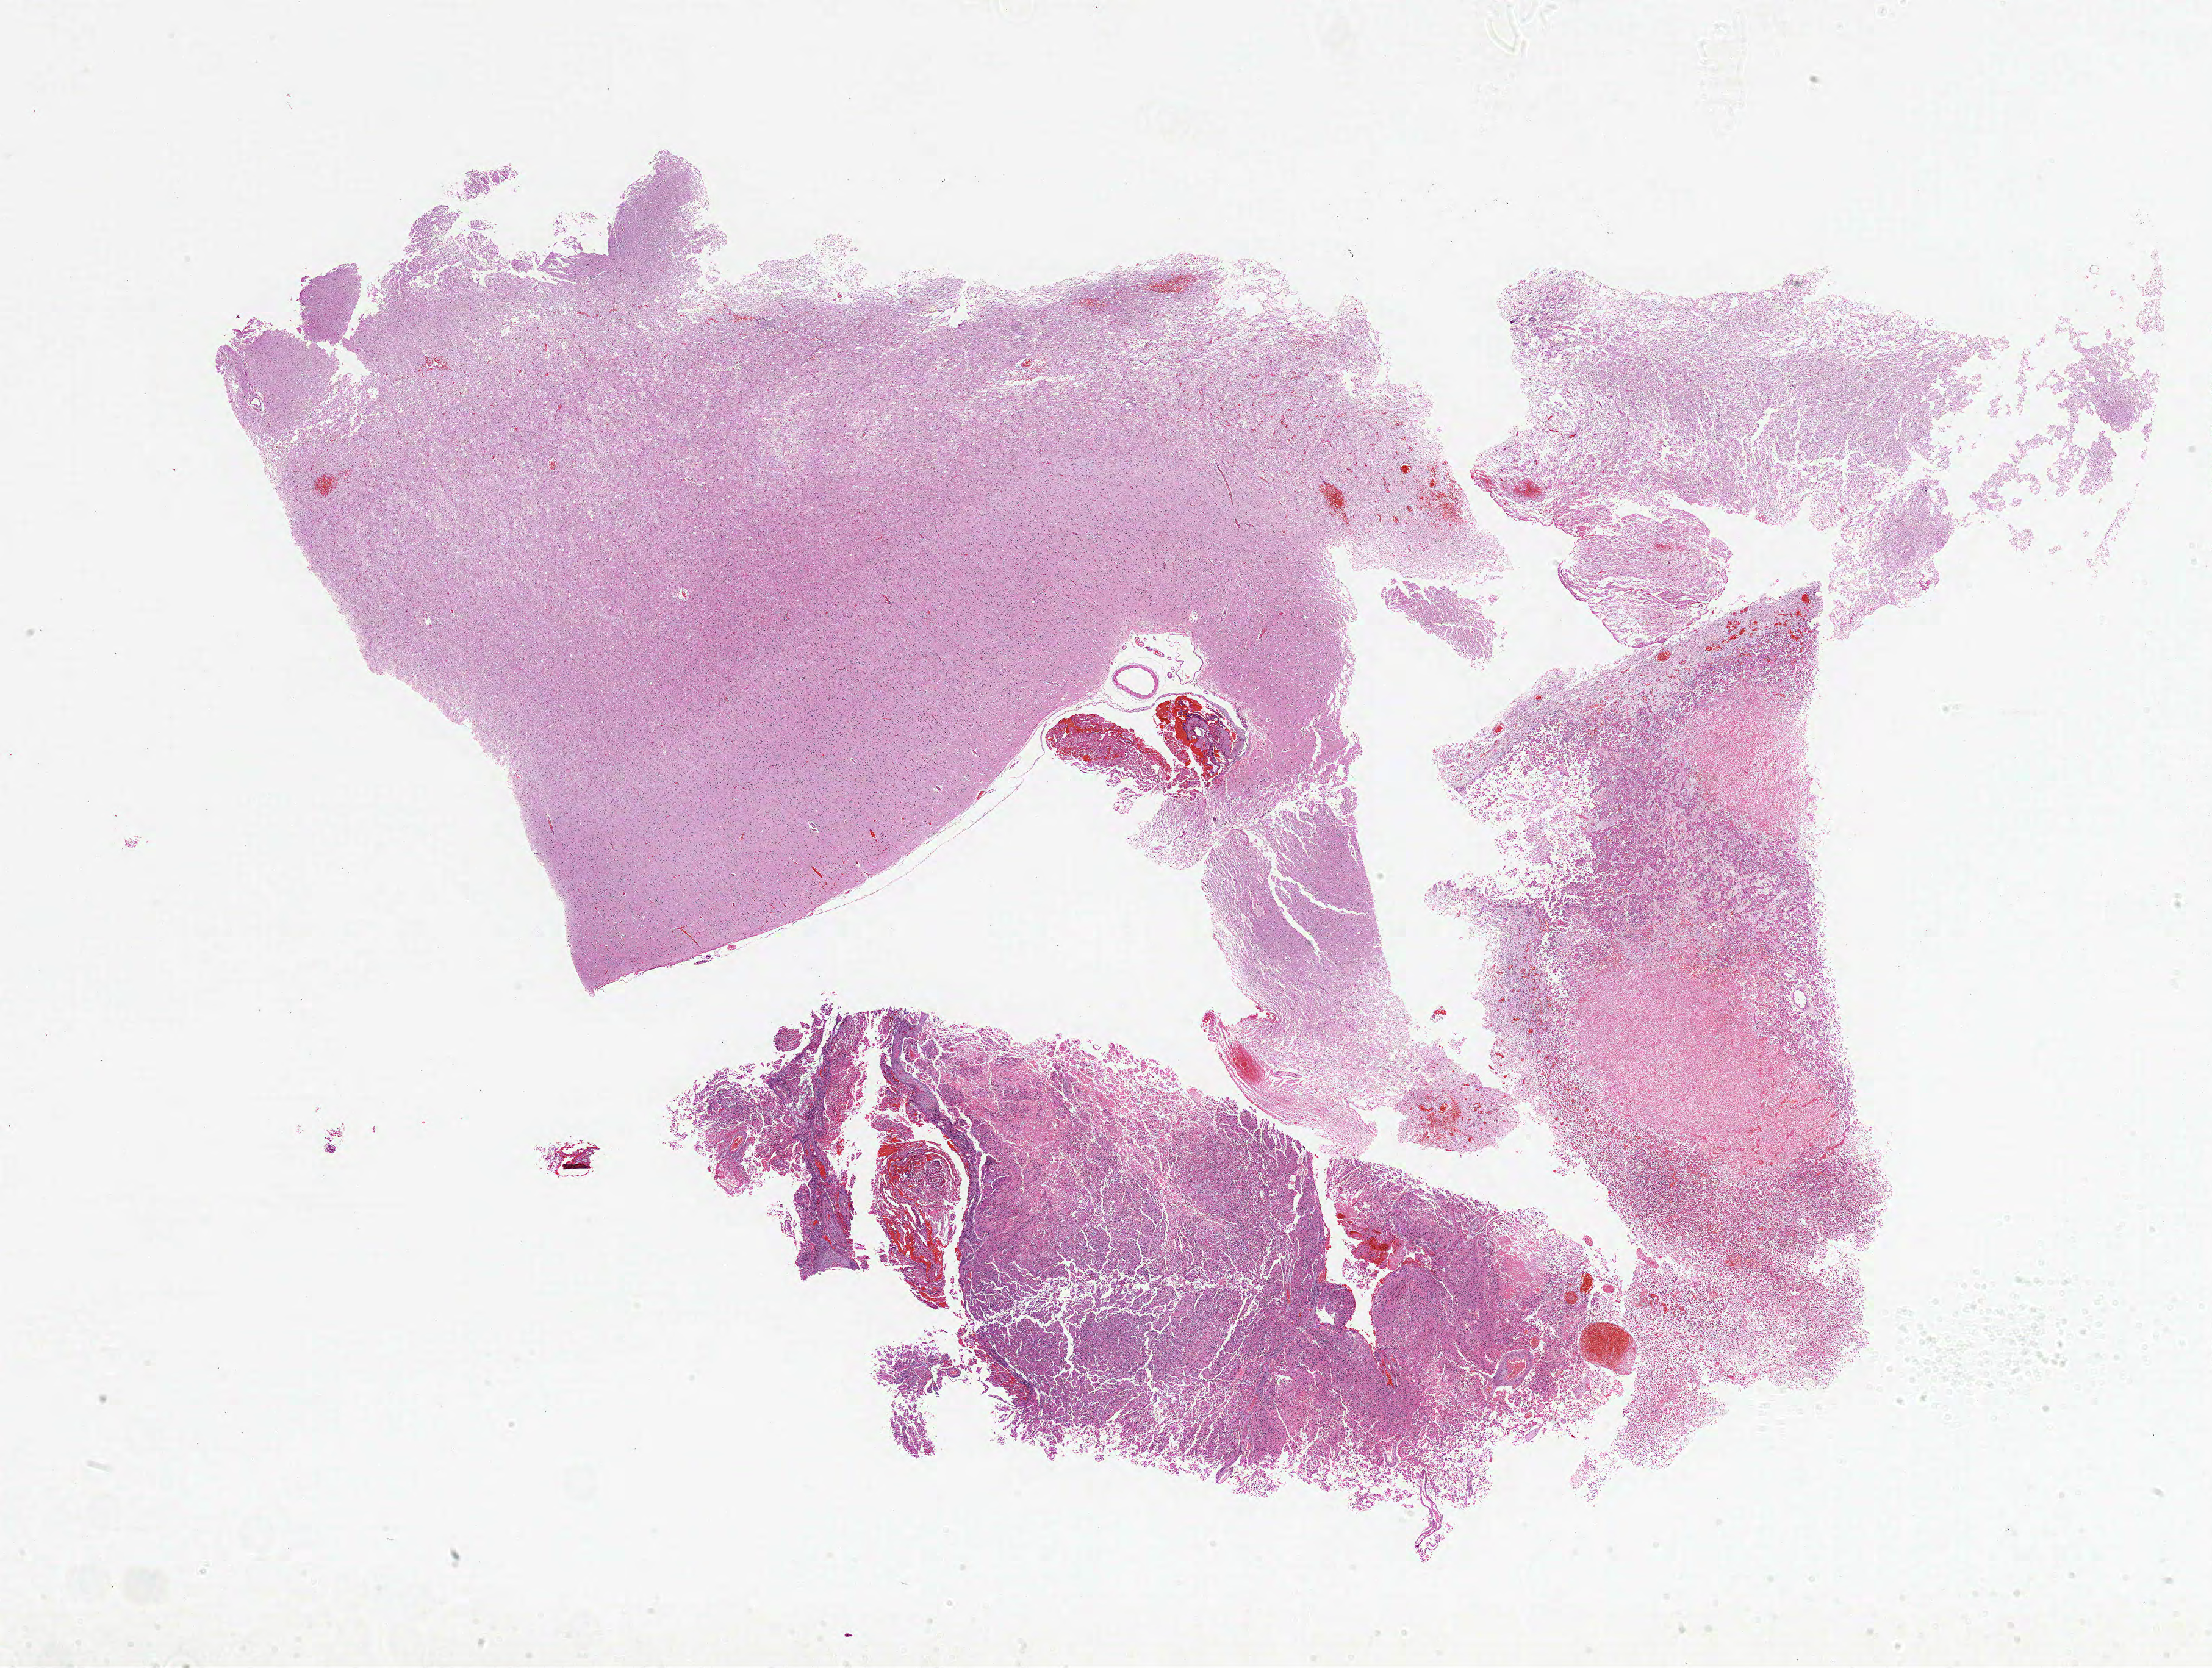
H&E whole-slide image, low-resolution overview of the scanned area, about 29.0 x 21.9 mm (slide scanned at 20x), FFPE section, brain, primary tumour sample. Patient: male, age at initial diagnosis 64 years.
Pathologic diagnosis: Glioblastoma.